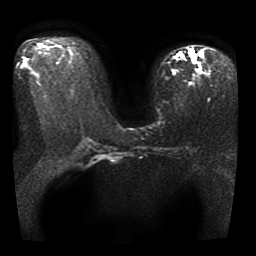
Breast MRI, one axial slice. Diffusion-weighted series; image 2 of 4 stored at this slice position (different b-values; order by instance number). 1.5 T. 5 mm slice thickness. 256 × 256 image matrix, field of view 330 × 330 mm. Female patient.
Structures marked on this image (expert manual segmentation):
- tumour on diffusion-weighted imaging: bounding box [x1, y1, x2, y2] px = [188, 50, 194, 59]